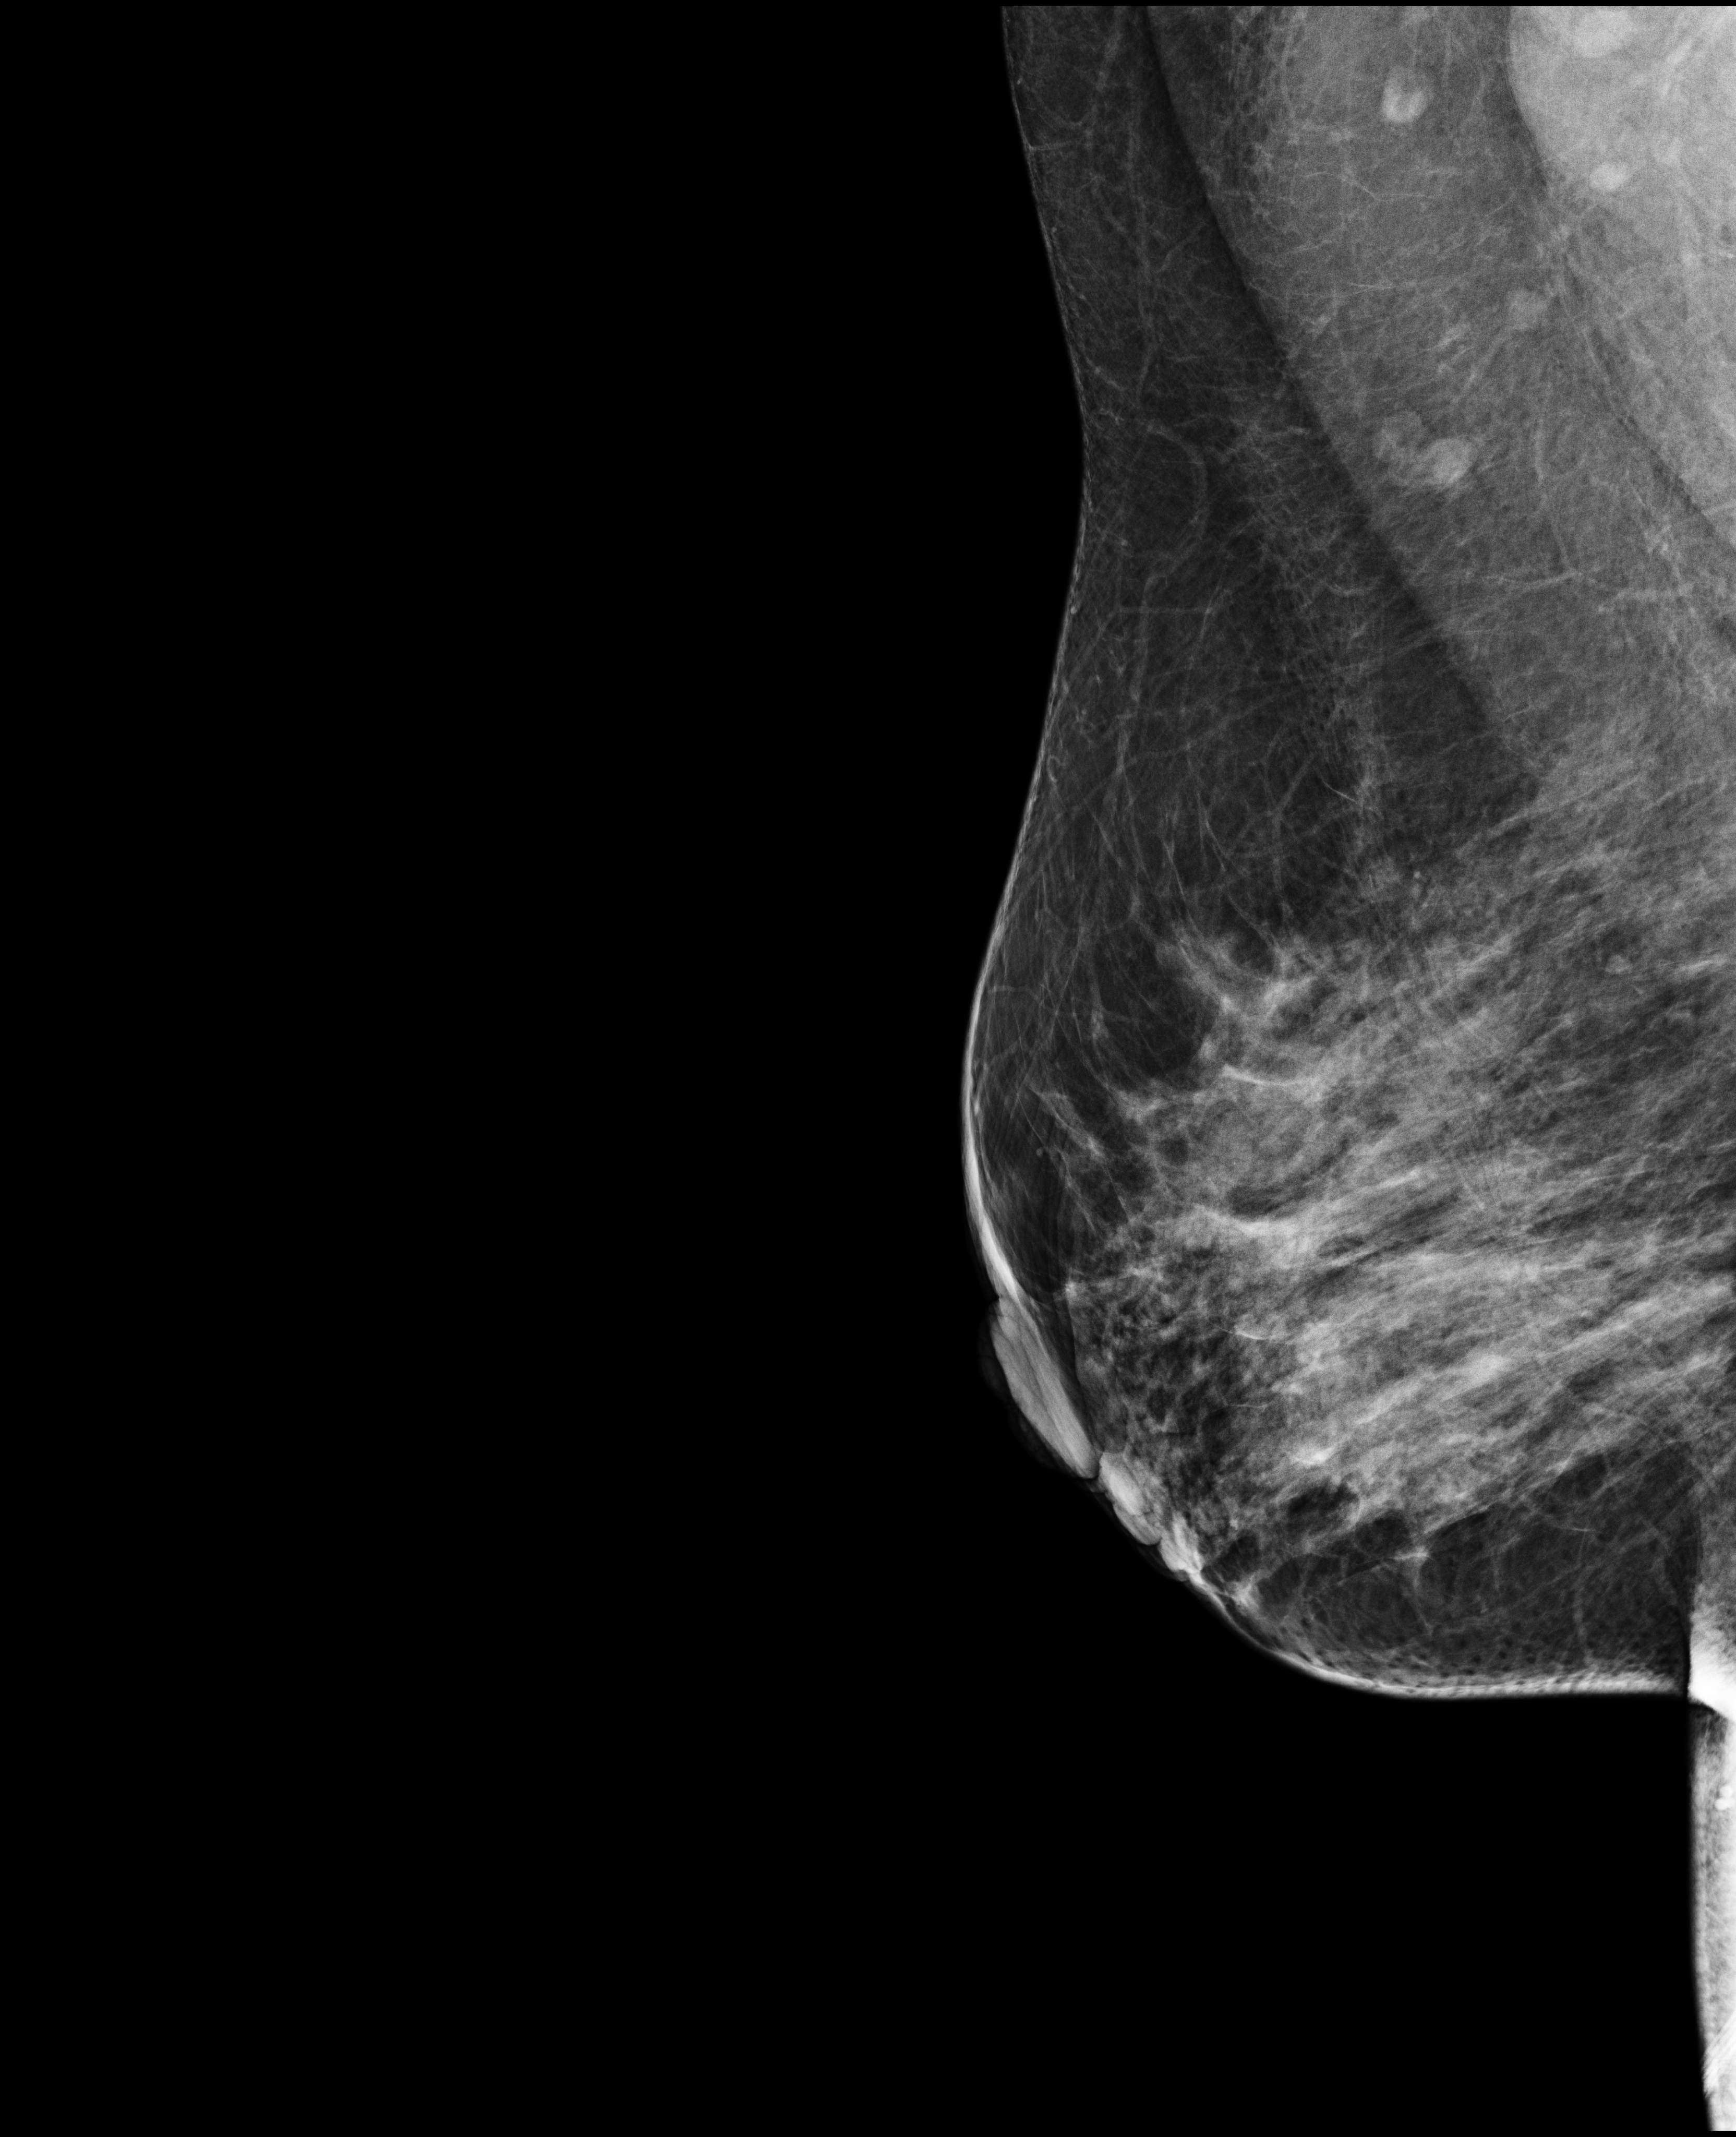
Annual screening mammography examination, compressed breast thickness 65 mm, system: Selenia Dimensions. Patient: female, 43 years.
Image type: full-field digital mammogram. Breast: right. Projection: mediolateral oblique (MLO) view.